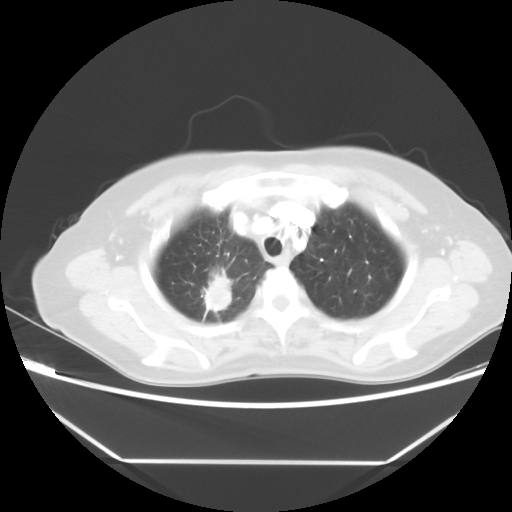
Chest CT, one axial slice. Position 41 of 48 along the scan axis. Reconstruction kernel STANDARD. 100 kVp. Lung window (W 1500 / L -600 HU). 5 mm slice thickness. 512 × 512 image matrix, field of view 360 × 360 mm. Female patient, age 65 years. Case-level facts recorded for this patient, not image findings: clinical TNM (as recorded): T1c N1 M1.
Outlined on this slice (bounding box drawn by a radiologist):
- lung tumour (recorded histology: adenocarcinoma): bounding box [x1, y1, x2, y2] px = [201, 267, 235, 312]